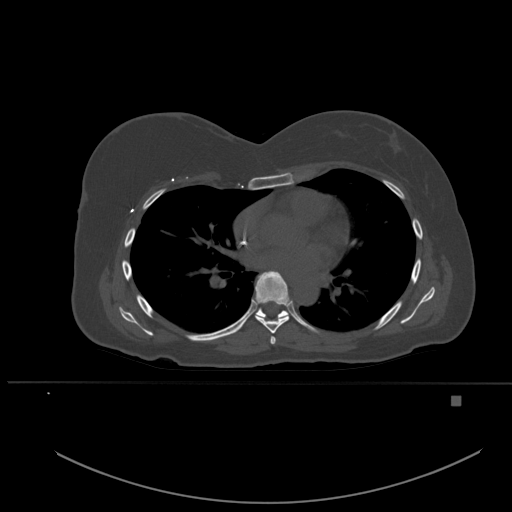
CT including the spine, one axial slice; position 345 of 651 along the scan axis; bone window (W 1800 / L 400 HU); 512 × 512 image matrix, field of view 443 × 443 mm. Patient: female, 49 years. Case-level facts recorded for this patient, not image findings: primary cancer: breast.
Annotated regions visible in this slice (semi-automatically segmented with operator editing):
- T5 vertebra: bounding box (x1, y1, x2, y2) in pixels: (270, 336, 276, 344)
- T6 vertebra: (255, 271, 291, 334)
- T7 vertebra: (255, 308, 289, 319)